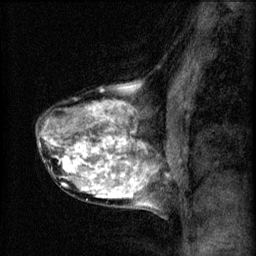
Breast MRI (dynamic contrast-enhanced), one sagittal slice; slice 38 of 60 in the series (ordered by position); 3 images stored at this slice position (order not interpretable as contrast timing); 1.5 T; TE 4.2 ms, TR 8.2 ms; 2 mm slice thickness; 256 × 256 image matrix, field of view 180 × 180 mm. Patient: female, 40 years.
Structures marked on this image (semi-automatic segmentation, software-assisted and operator-edited):
- analysis volume of interest (the breast-tissue region the enhancement analysis was run in; not a lesion): bounding box <35,80,167,211> (left, top, right, bottom; pixels)
- tumour enhancement mask (voxels above the 70 % enhancement threshold inside the analysis volume of interest): <45,84,156,209>